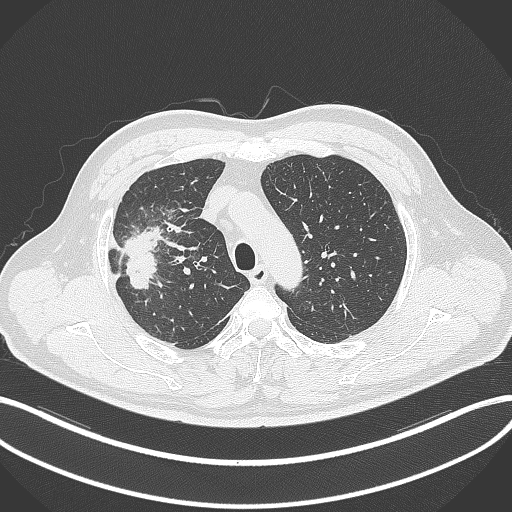
Chest CT, one axial slice; slice 258 of 348 in the series (ordered by position); 120 kVp; lung window (W 1500 / L -600 HU); 1 mm slice thickness; 512 × 512 image matrix. Patient: male, 55 years. From the clinical record (not read from this slice): clinical TNM (as recorded): T3 N2 M1.
Outlined on this slice (bounding box drawn by a radiologist):
- lung tumour (recorded histology: adenocarcinoma): bounding box [x1, y1, x2, y2] px = [120, 220, 163, 293]